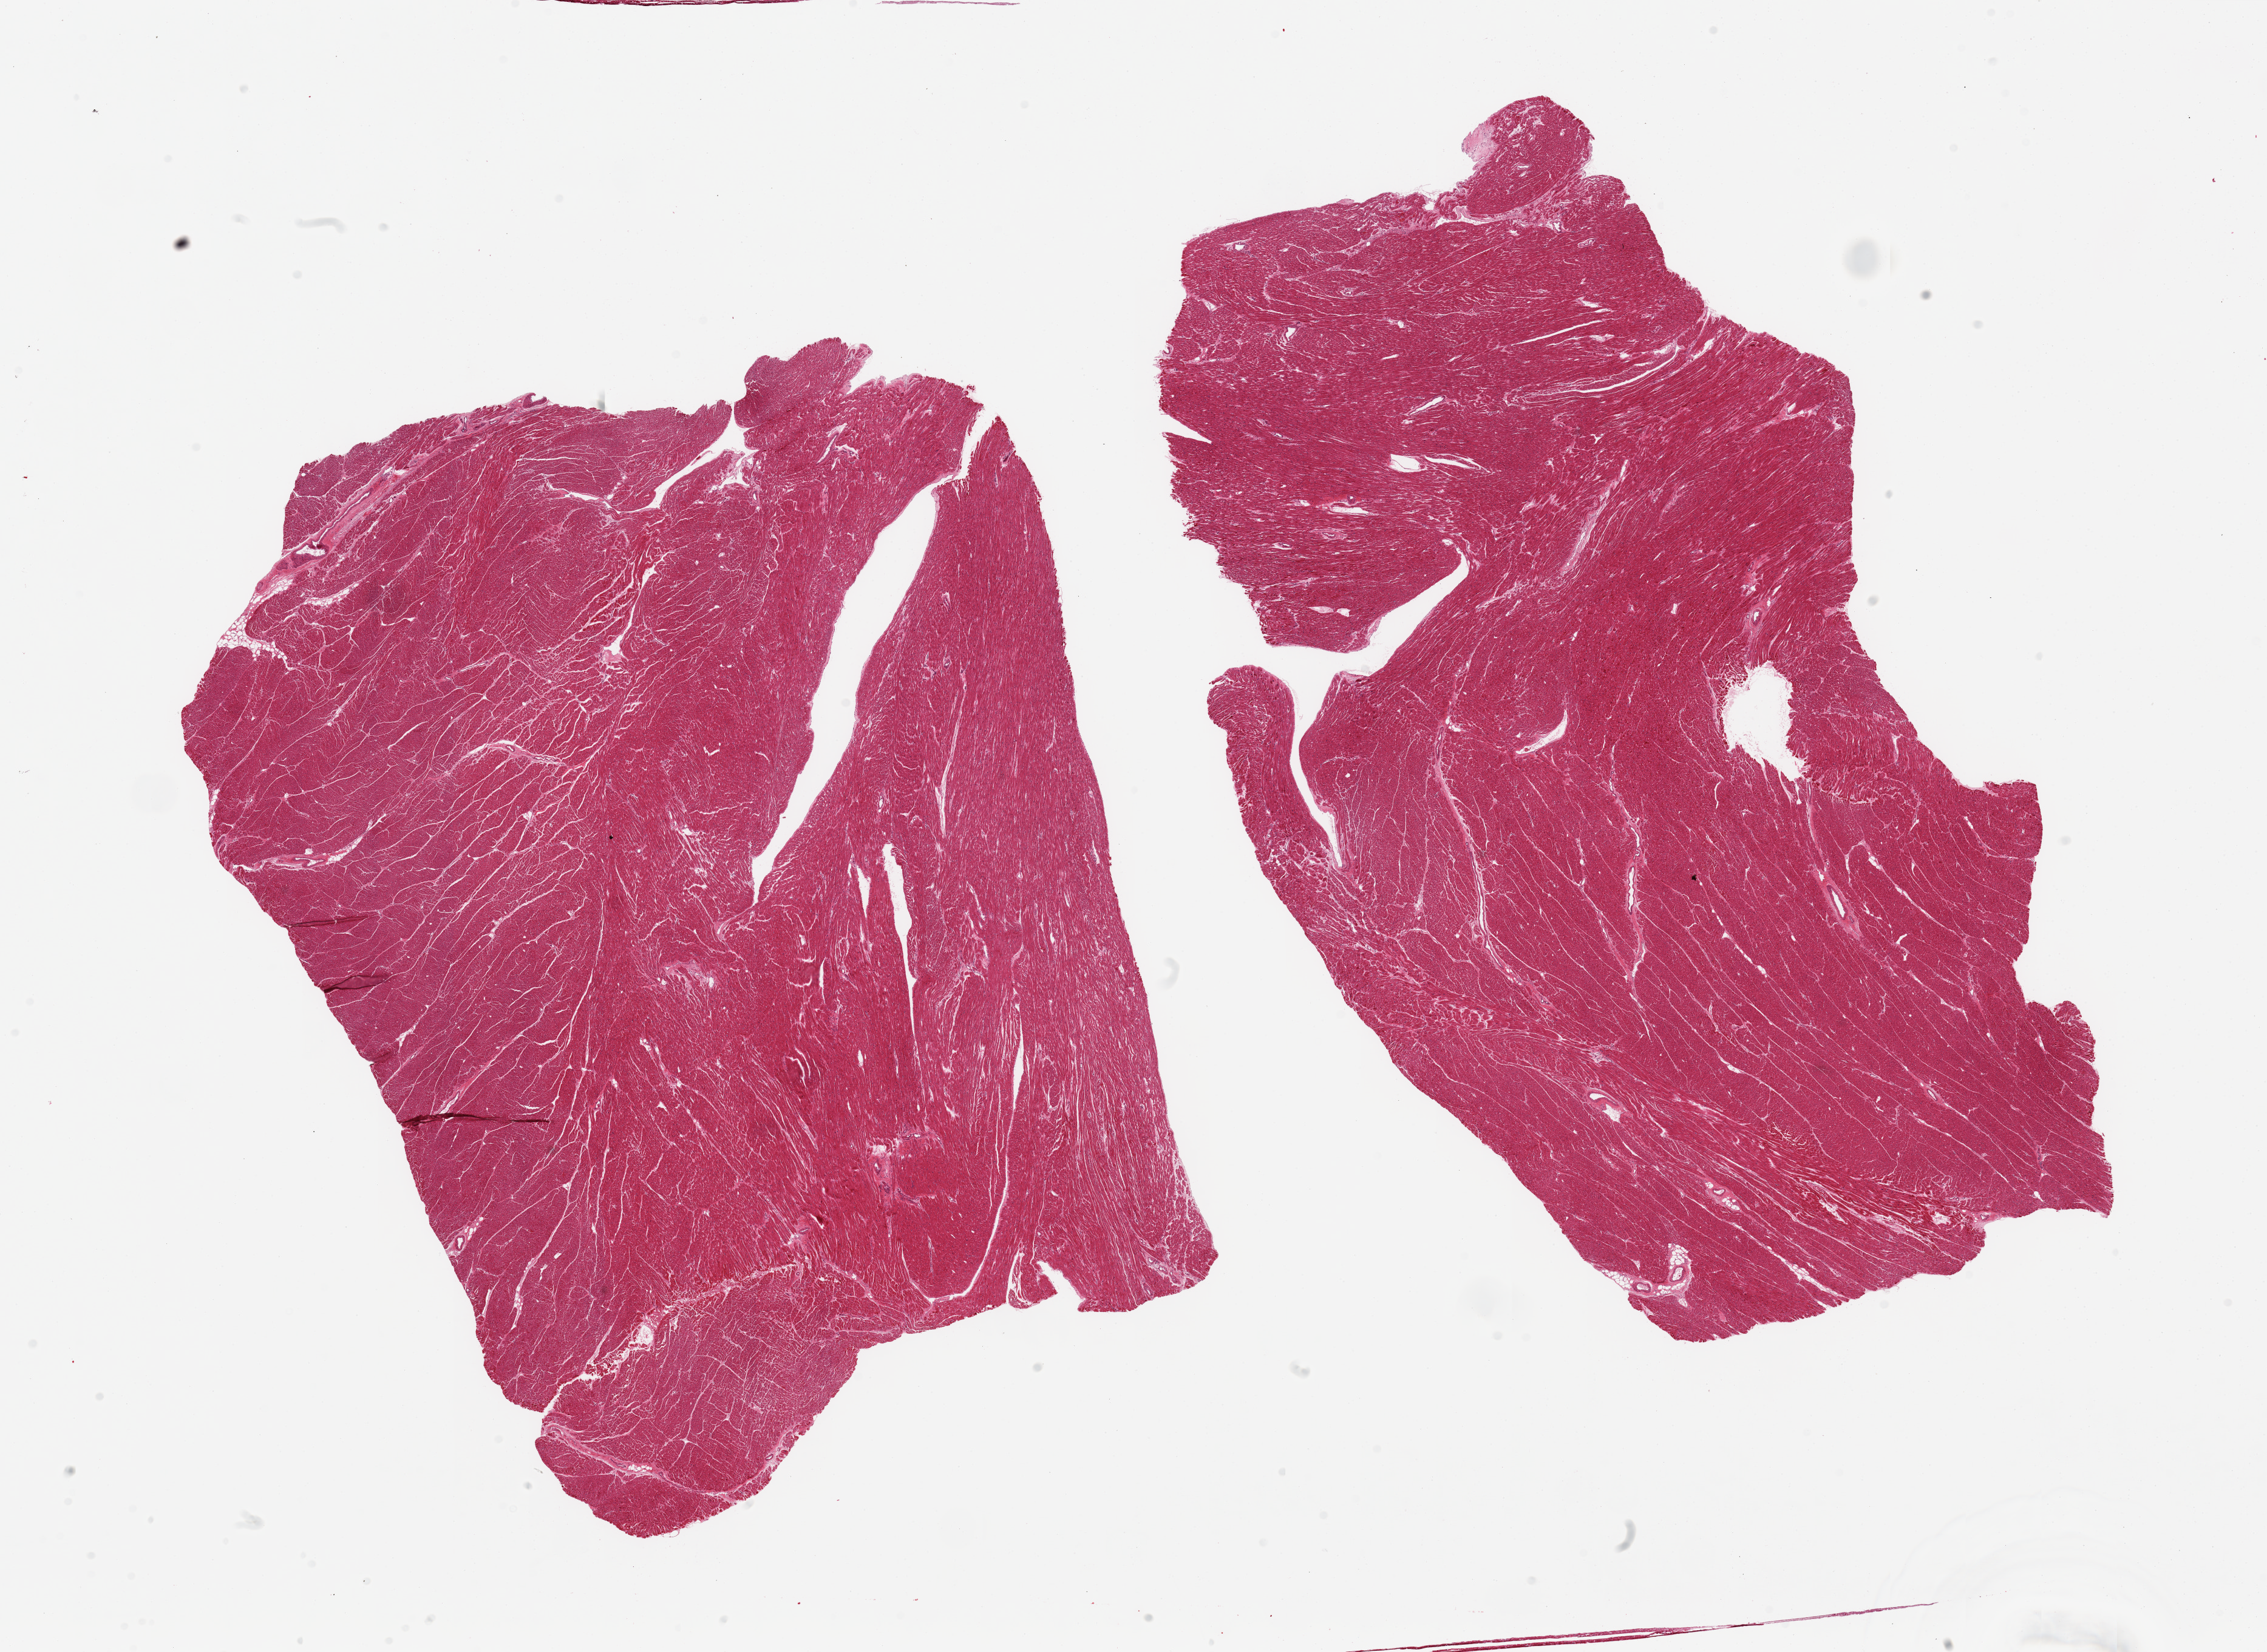
Whole-slide image, H&E stain, a low-resolution overview of the entire scanned area, about 29.5 x 21.5 mm, PAXgene-fixed paraffin-embedded (PFPE) section, sampled site (target tissue): heart, tissue donor sample. Donor: male.
Reviewer comment on this tissue sample: 2 pieces.